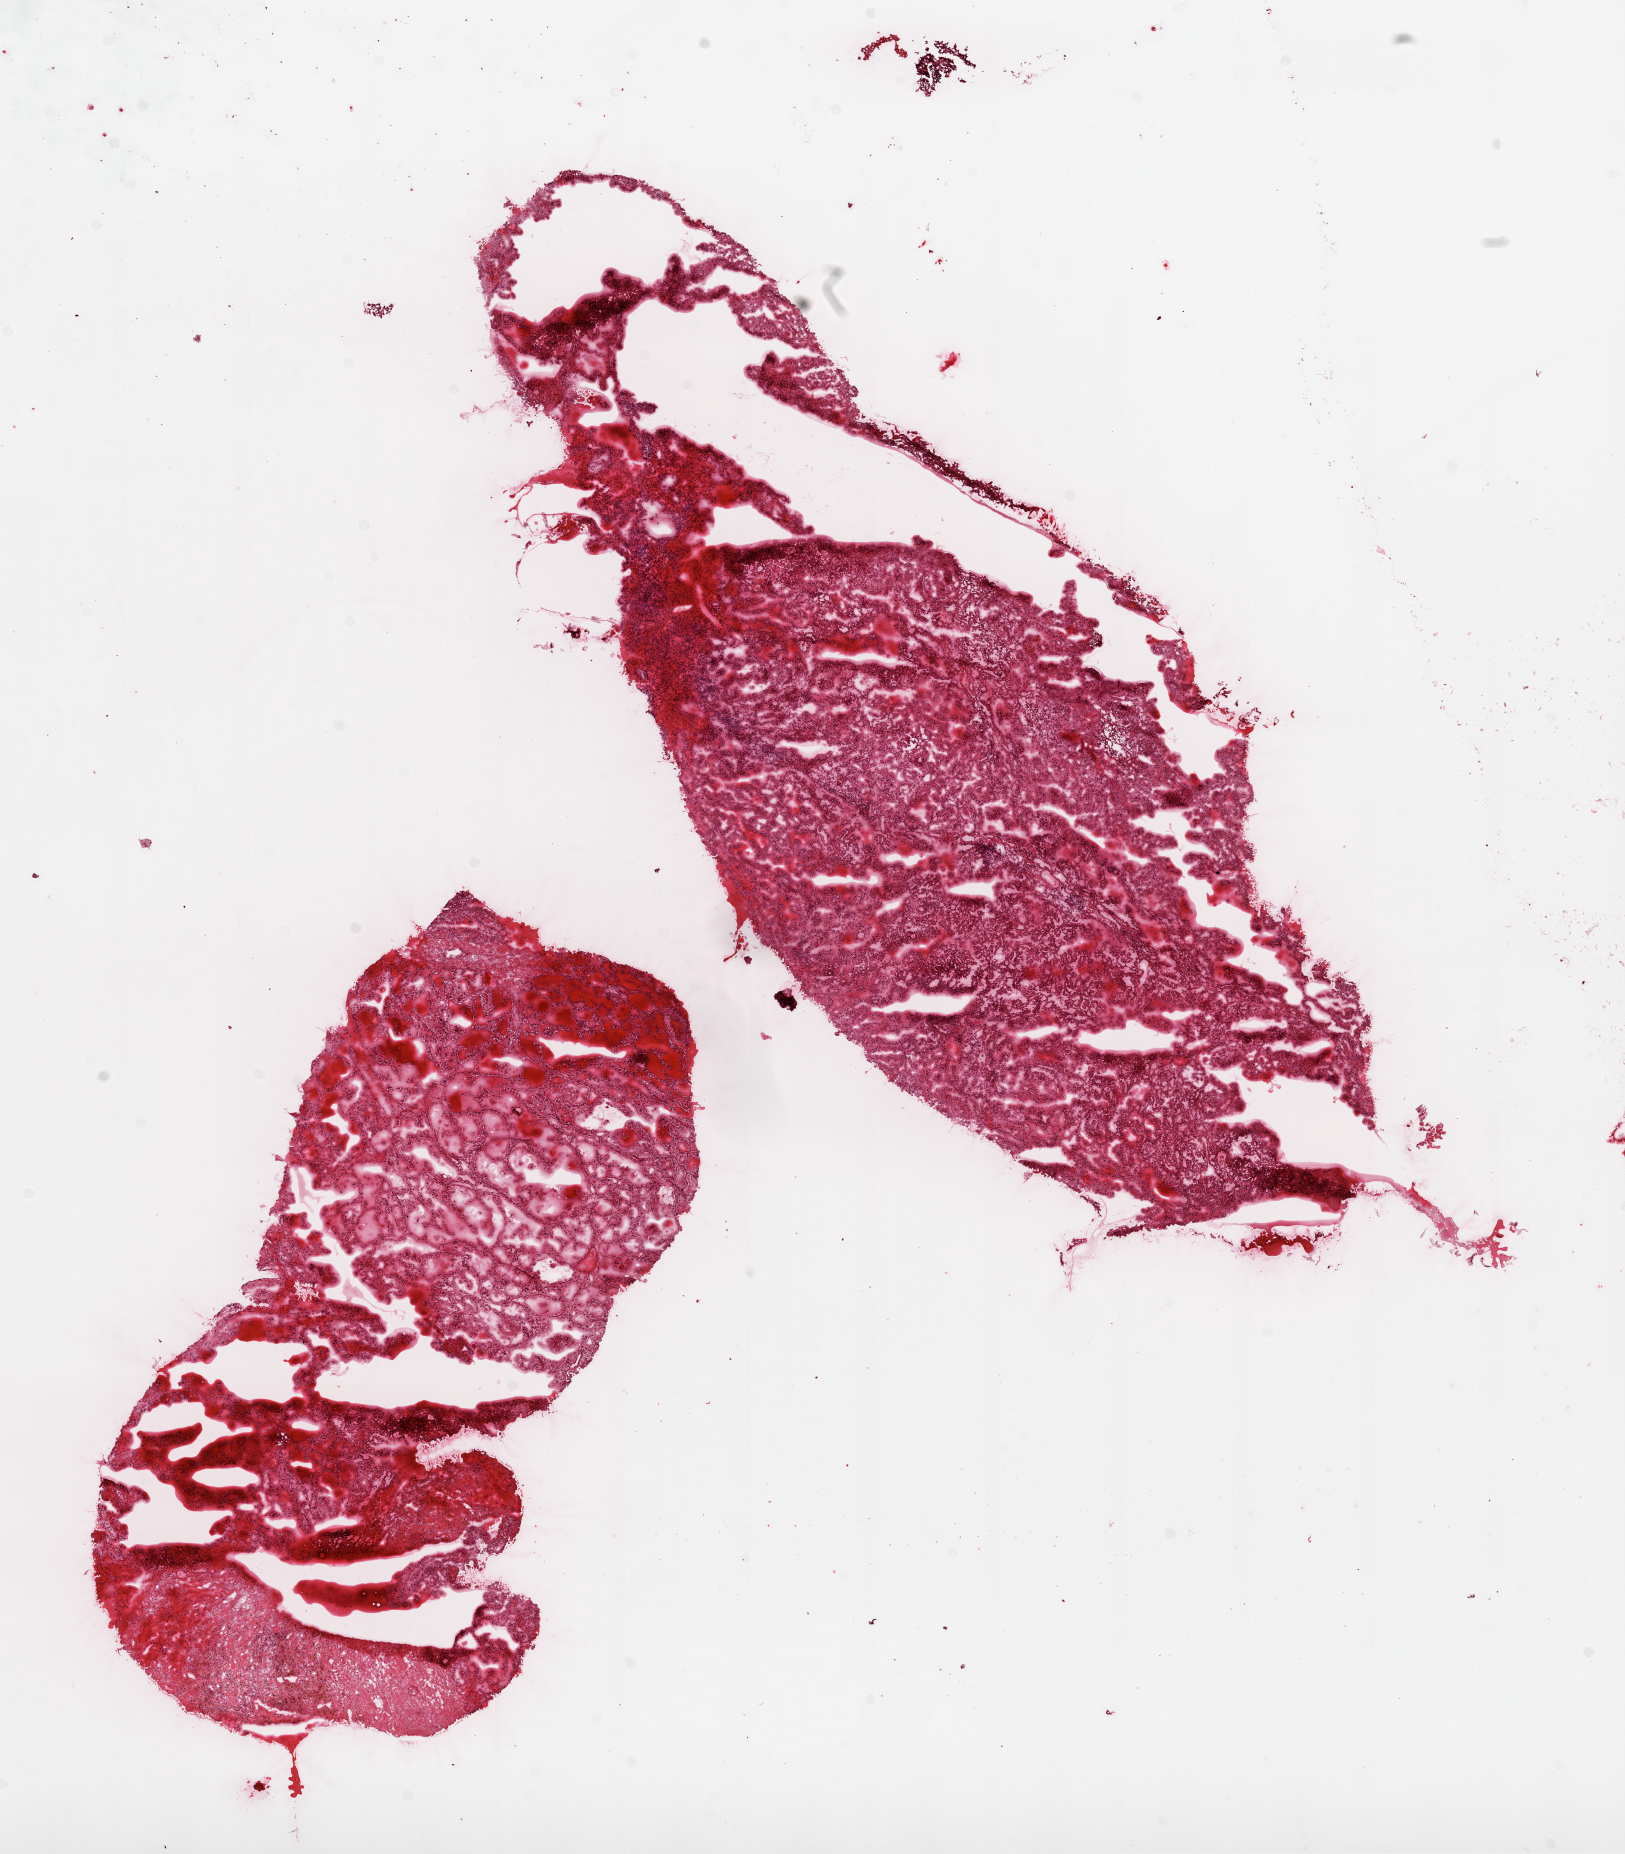
Digitized Hematoxylin and eosin (H&E) stained tissue section (whole slide) — low-resolution overview of the scanned area, about 13.0 x 14.9 mm (acquisition: 20x scan), frozen section from the top of the tissue portion, primary tumour sample from the kidney. Male, age 46 years at initial diagnosis. Histologic grade: G3 (poorly differentiated). Slide review estimates, as recorded: tumour cells 100%, tumour nuclei 90%, necrosis 0%. Inflammatory infiltration, as recorded: lymphocyte infiltration 5%.
Laterality: right. AJCC pathologic stage: I. Pathologic diagnosis: Clear cell adenocarcinoma, NOS.